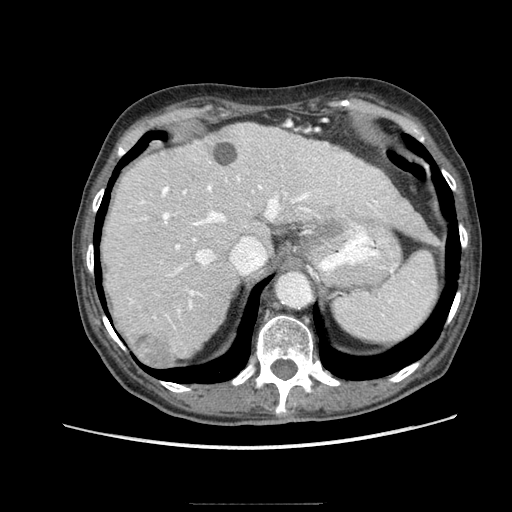
Contrast-enhanced abdominal CT (liver protocol), one axial slice; position 63 of 83 along the scan axis; 140 kVp; soft-tissue window (W 400 / L 40 HU); 2.5 mm slice thickness; 512 × 512 image matrix. From the clinical record (not read from this slice): diagnosis: hepatocellular carcinoma (patient treated with transarterial chemoembolisation; whether this scan precedes or follows treatment is not stated here); TNM stage (as recorded): Stage-I; Child-Pugh class: A.
Outlined on this slice (semi-automatic segmentation, software-assisted and operator-edited):
- abdominal aorta: bounding box (x1, y1, x2, y2) in pixels: (276, 272, 313, 308)
- liver parenchyma outside the tumour (the mass and vessels are separate outlines, so this box may not span the whole liver): (102, 122, 426, 358)
- mass: (134, 333, 176, 368)
- liver vessels: (131, 130, 378, 313)